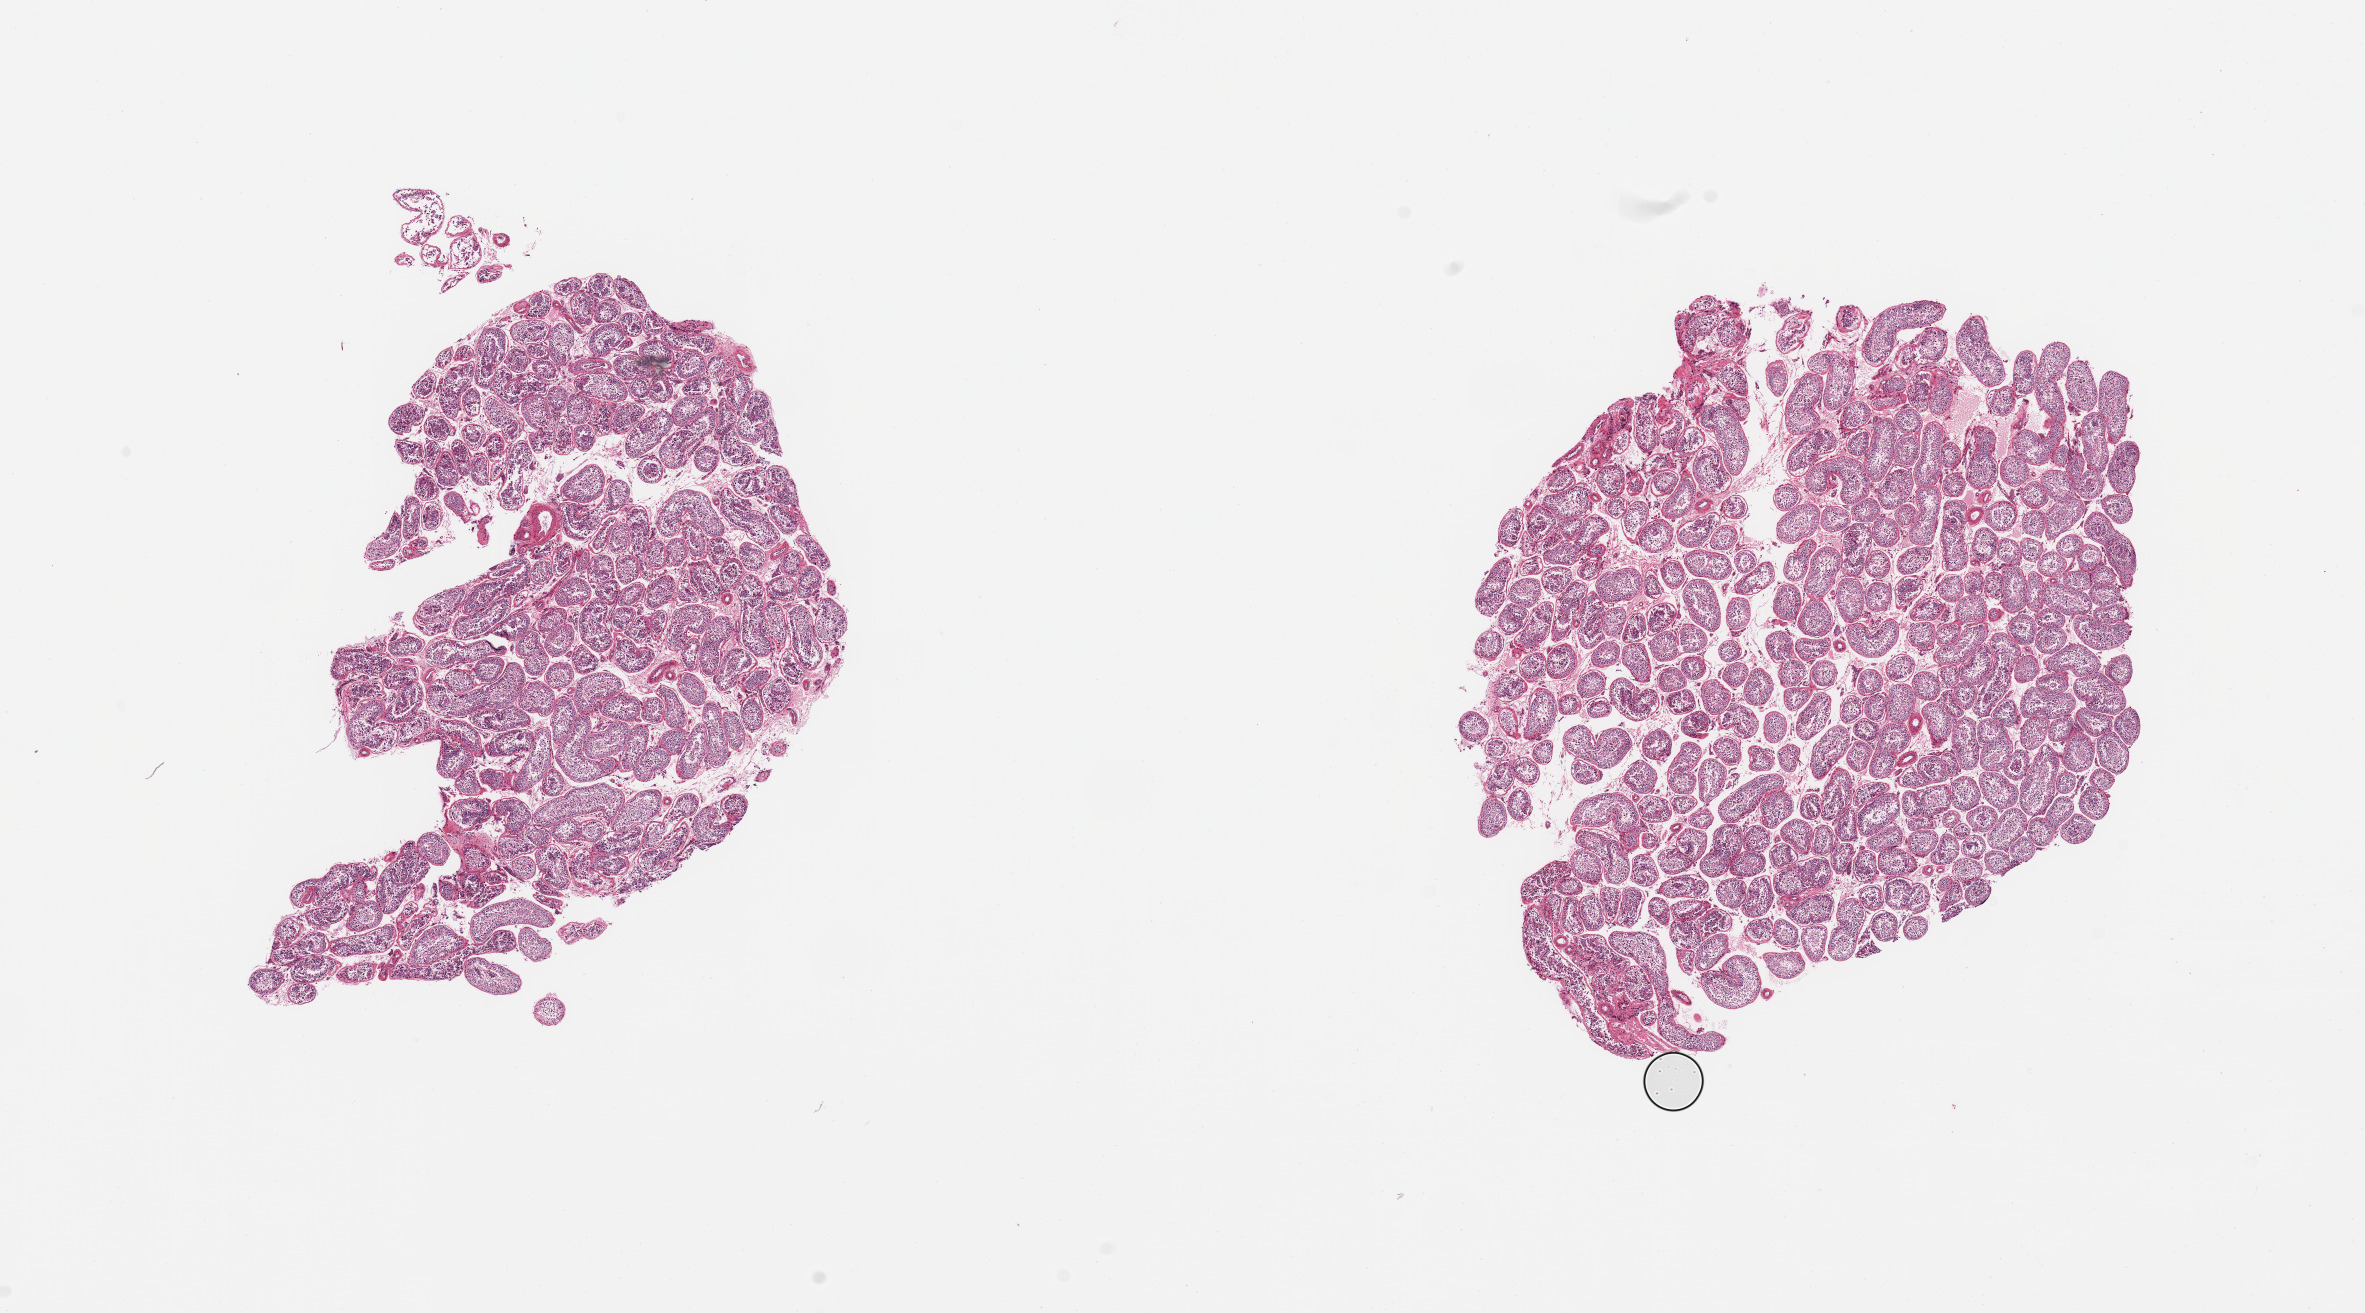
Digitized haematoxylin and eosin-stained section — whole scanned area (about 18.7 x 10.4 mm, acquisition: 20x scan) shown as a low-resolution overview, PAXgene-fixed, paraffin-embedded tissue, target tissue: testis, donor tissue sample.
• pathologist's review note for this sample: 2 pieces; active spermatogenesis